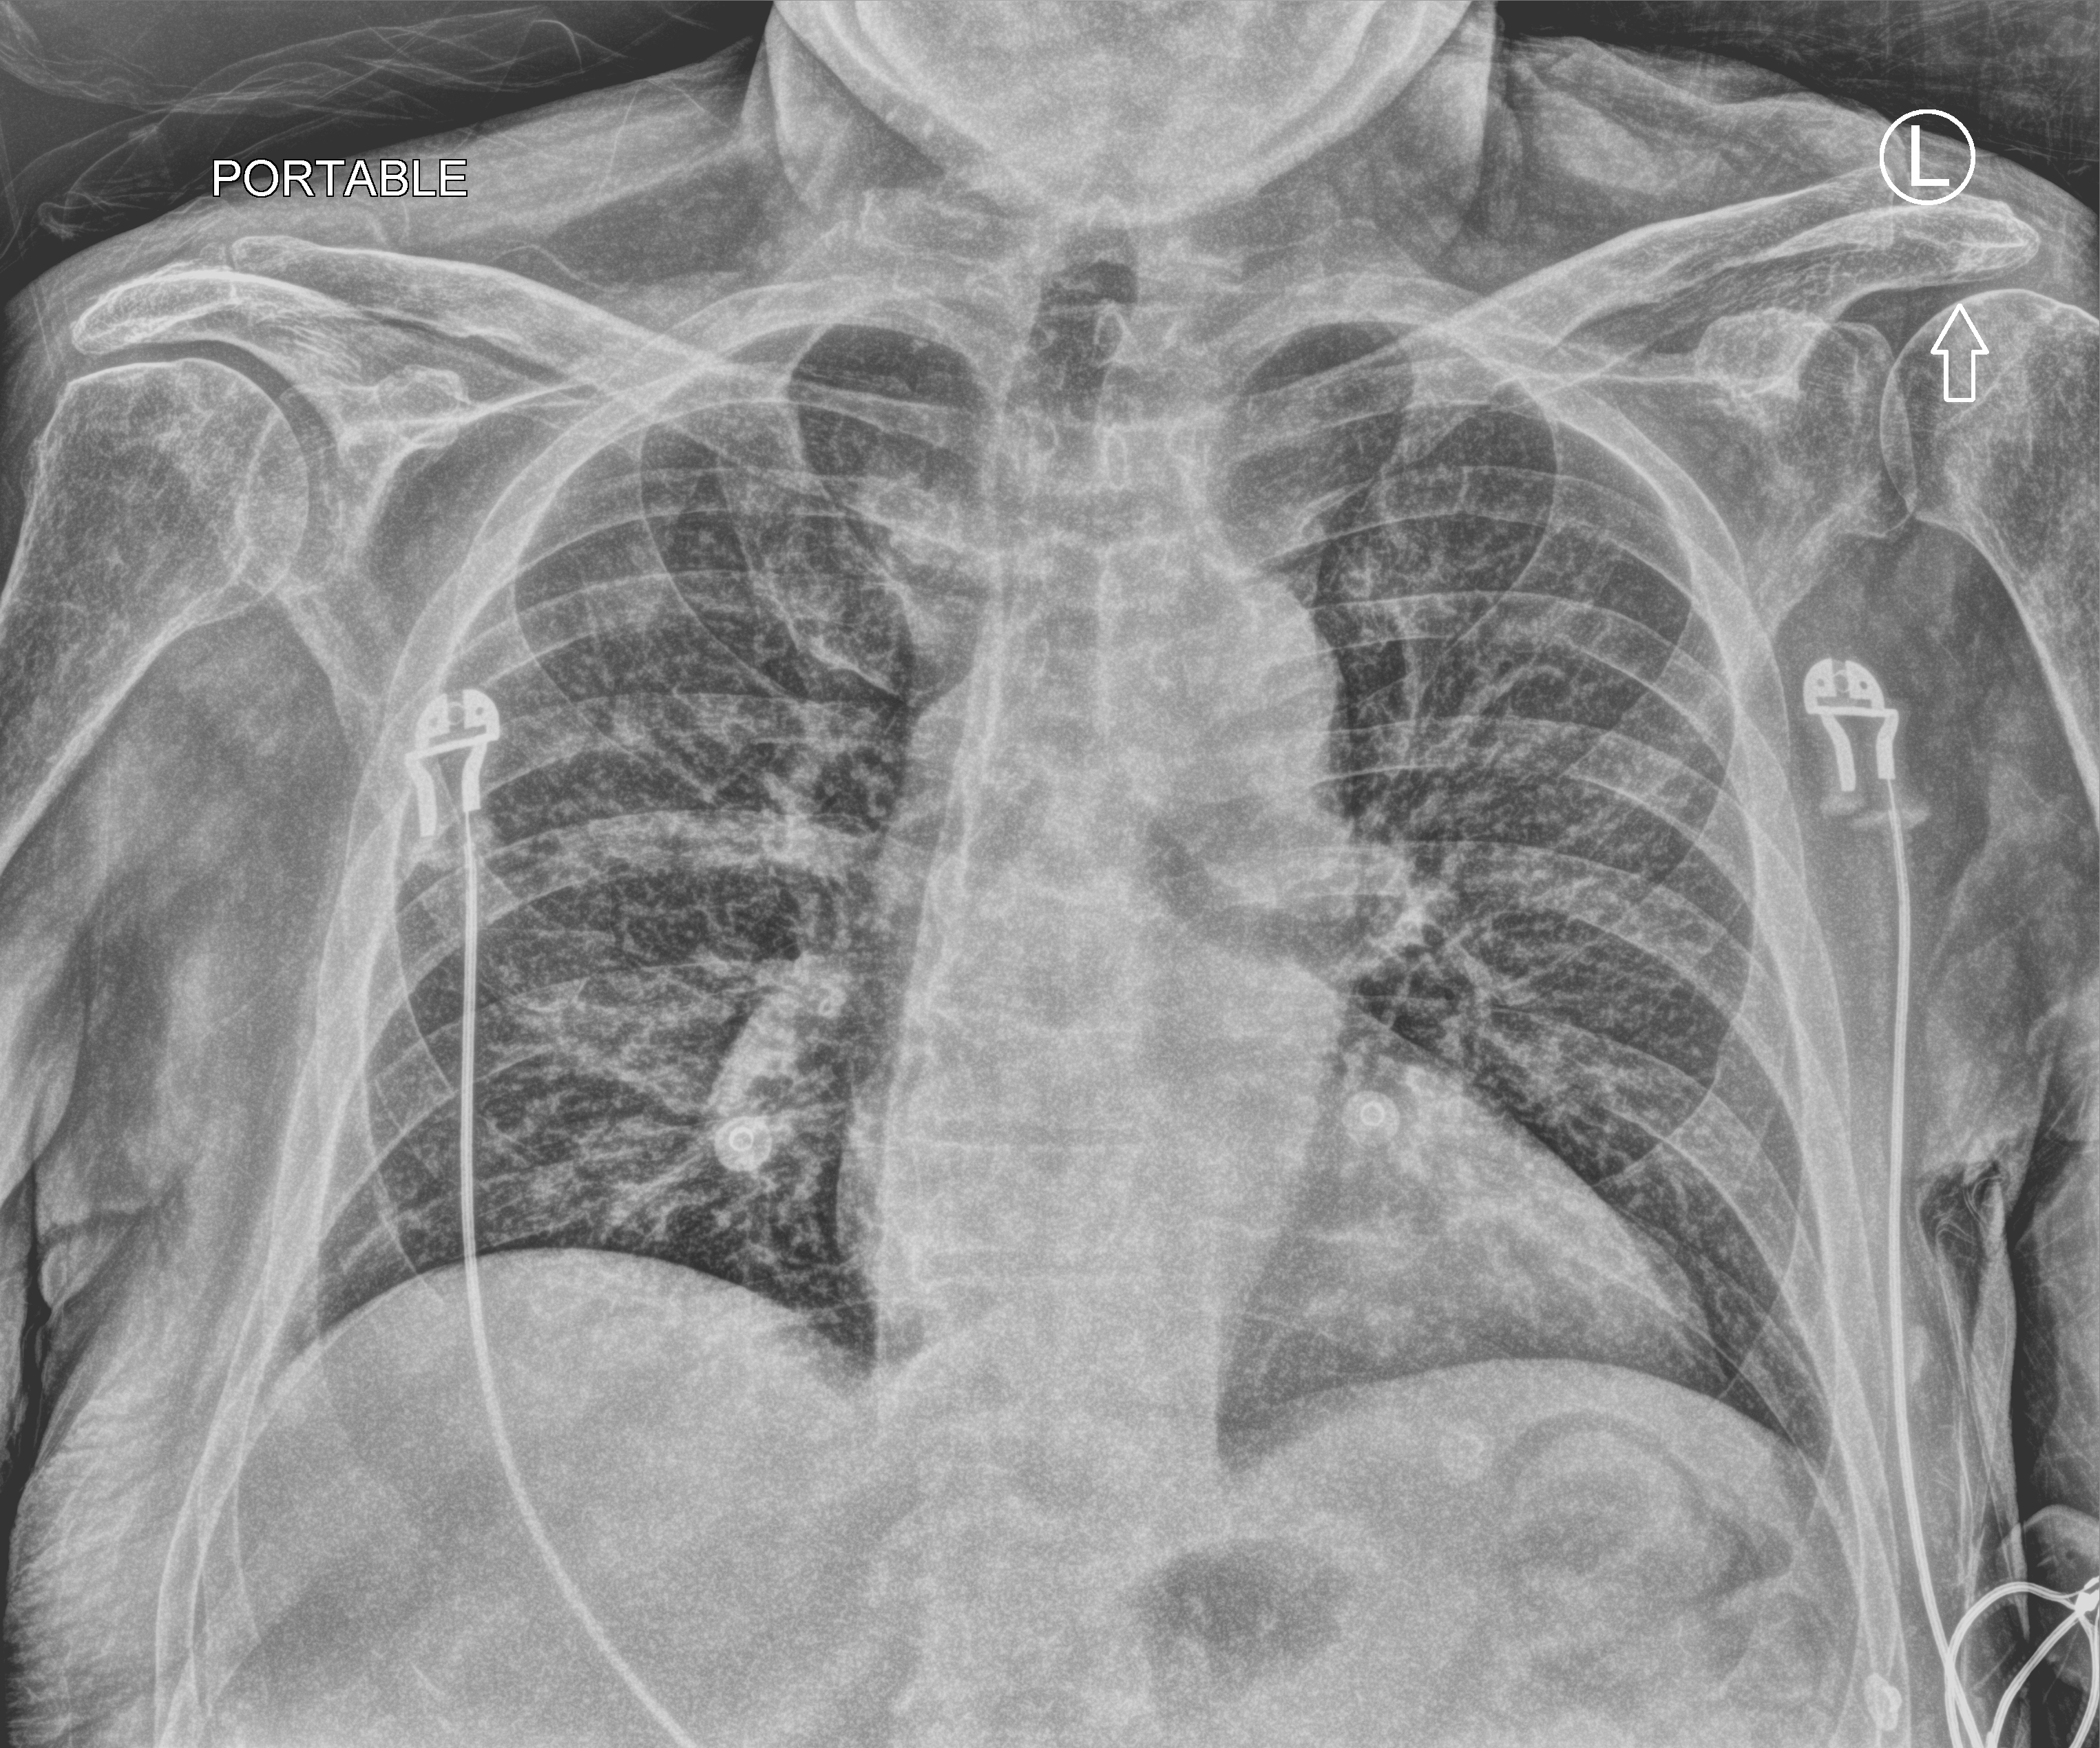
Chest X-ray (portable), anteroposterior (AP) projection. Patient hospitalised with COVID-19; male, aged 60–74 years.
Admission-level facts for this patient (not findings on this image; timing relative to this image not recorded):
- admitted to intensive care during this hospital stay: no
- mechanically ventilated during this hospital stay: no
- length of hospital stay: 4 days